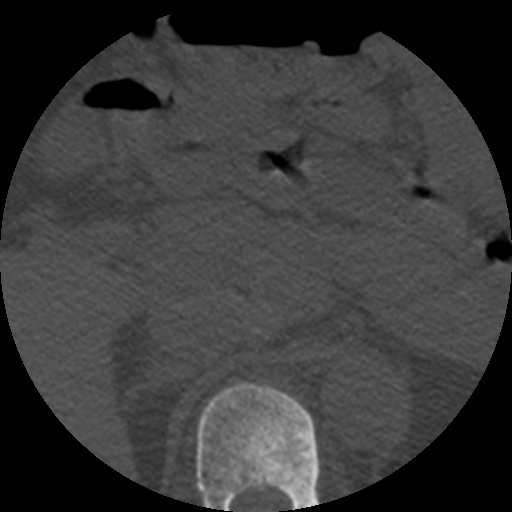
CT including the spine, one axial slice; slice 241 of 508 in the series (ordered by position); reconstruction kernel STANDARD; 120 kVp; bone window (W 1800 / L 400 HU); 1.25 mm slice thickness; 512 × 512 image matrix, field of view 160 × 160 mm. Patient age 57 years. Case-level facts recorded for this patient, not image findings: primary cancer: prostate.
Annotated regions visible in this slice (semi-automatic segmentation, software-assisted and operator-edited):
- T11 vertebra: bounding box [x1, y1, x2, y2] px = [196, 382, 320, 512]